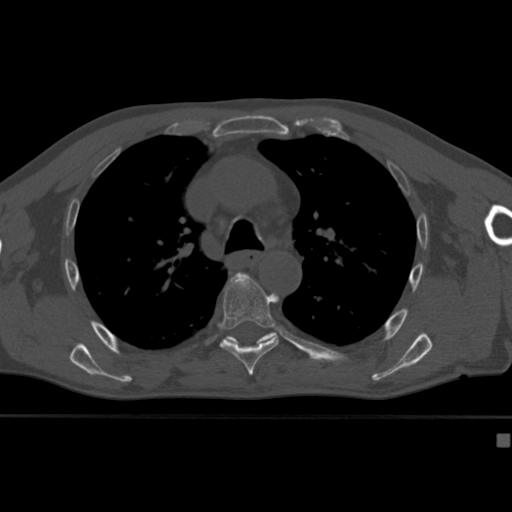
CT including the spine, one axial slice; slice 293 of 430 in the series (ordered by position); reconstruction kernel Br40s; 120 kVp; bone window (W 1800 / L 400 HU); 1.5 mm slice thickness; 512 × 512 image matrix, field of view 337 × 337 mm. Patient: male, 64 years. From the clinical record (not read from this slice): primary cancer: uterus; vertebrae with lytic lesions (as recorded): T1, T4, T5, T7, L5.
Annotated regions visible in this slice (semi-automatic segmentation, software-assisted and operator-edited):
- T5 vertebra: bounding box [x1, y1, x2, y2] px = [239, 273, 241, 275]
- T6 vertebra: [220, 273, 279, 376]
- T7 vertebra: [225, 332, 276, 345]